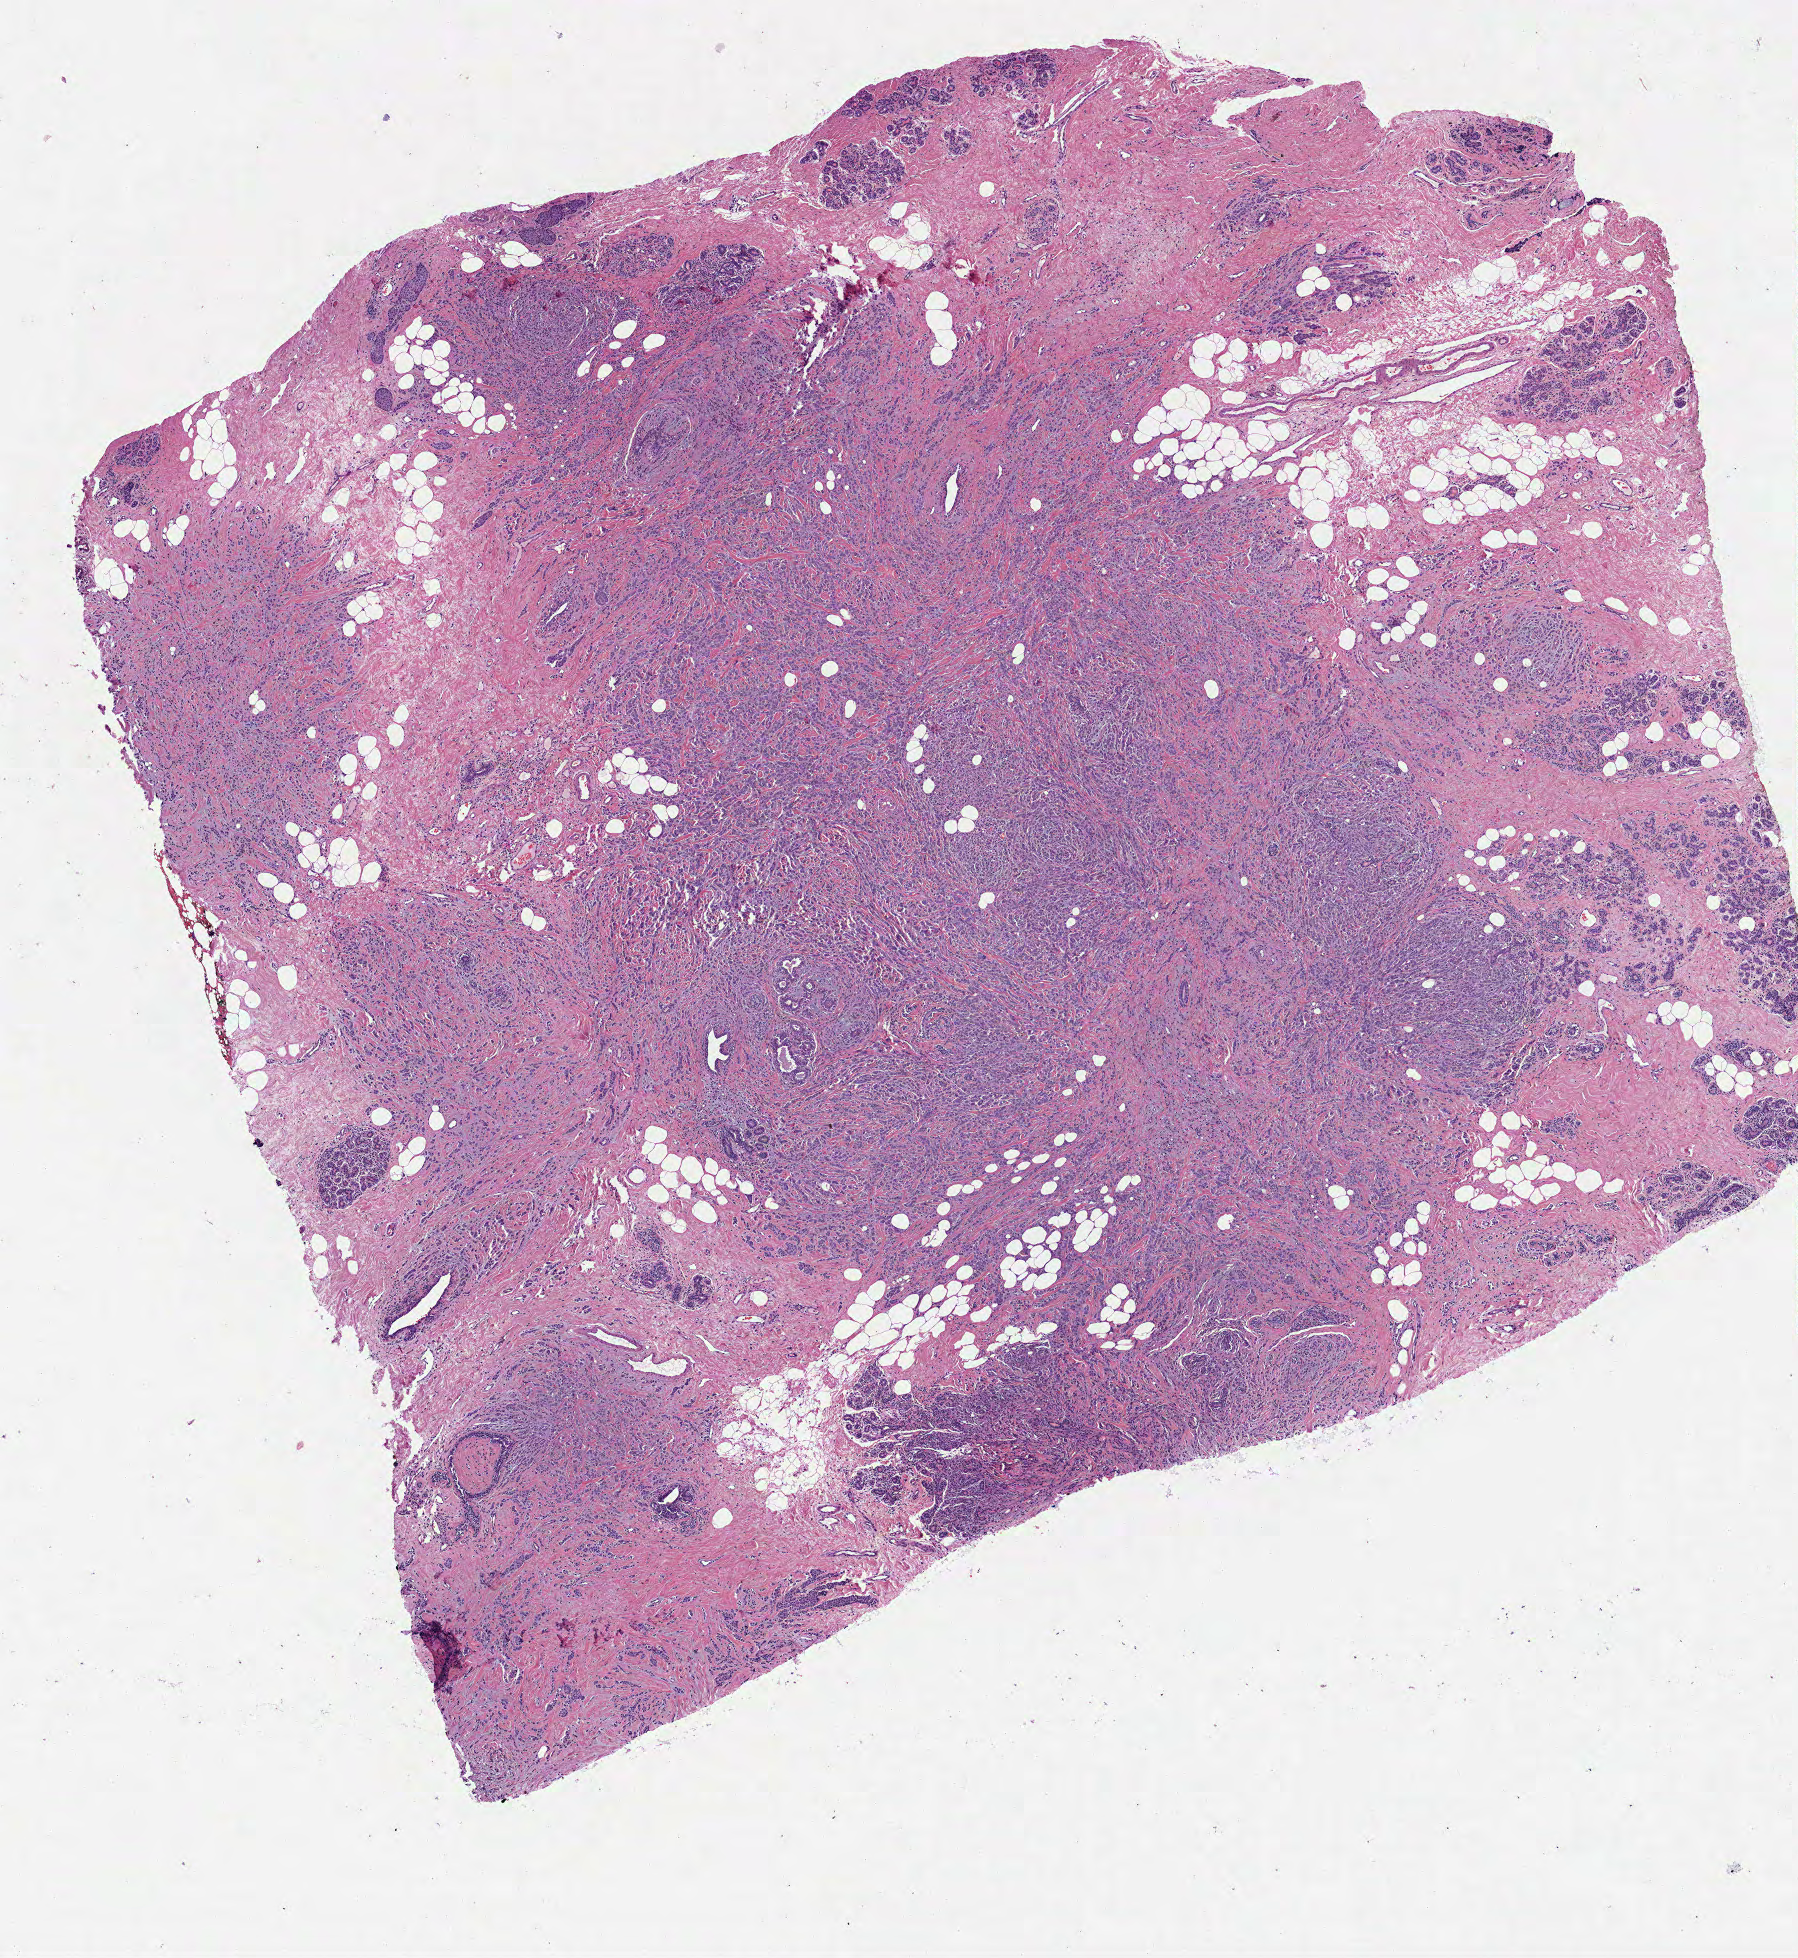
Whole-slide histology image, Hematoxylin and eosin (H&E) stained, shown as a low-resolution overview of the whole scanned area (about 7.3 x 7.9 mm). Formalin-fixed paraffin-embedded (FFPE) diagnostic section. Sample: primary tumour, breast. Female patient; age at initial diagnosis 45 years.
TNM: T2 N3a M0. Lymph nodes positive (case pathology): 3 of 3 examined. Diagnosis: Lobular carcinoma, NOS. AJCC pathologic stage: IIIC (6th edition).